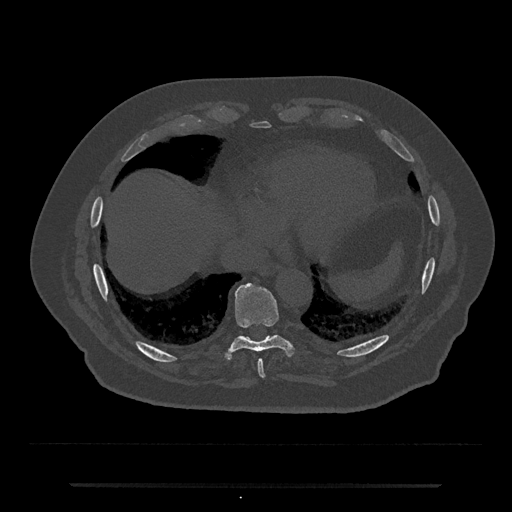
CT including the spine, one axial slice. Slice 756 of 797 in the series (ordered by position). Reconstruction kernel Br40s/3. 120 kVp. Bone window (W 1800 / L 400 HU). 0.5 mm slice thickness. 512 × 512 image matrix. Male patient, age 80 years. Case-level facts recorded for this patient, not image findings: primary cancer: prostate; vertebrae with lytic lesions (as recorded): L1, T11.
Structures marked on this image (semi-automatic segmentation, software-assisted and operator-edited):
- T8 vertebra: box from (x=257, y=360) to (x=265, y=378) px
- T9 vertebra: (x=227, y=282)–(x=292, y=358)